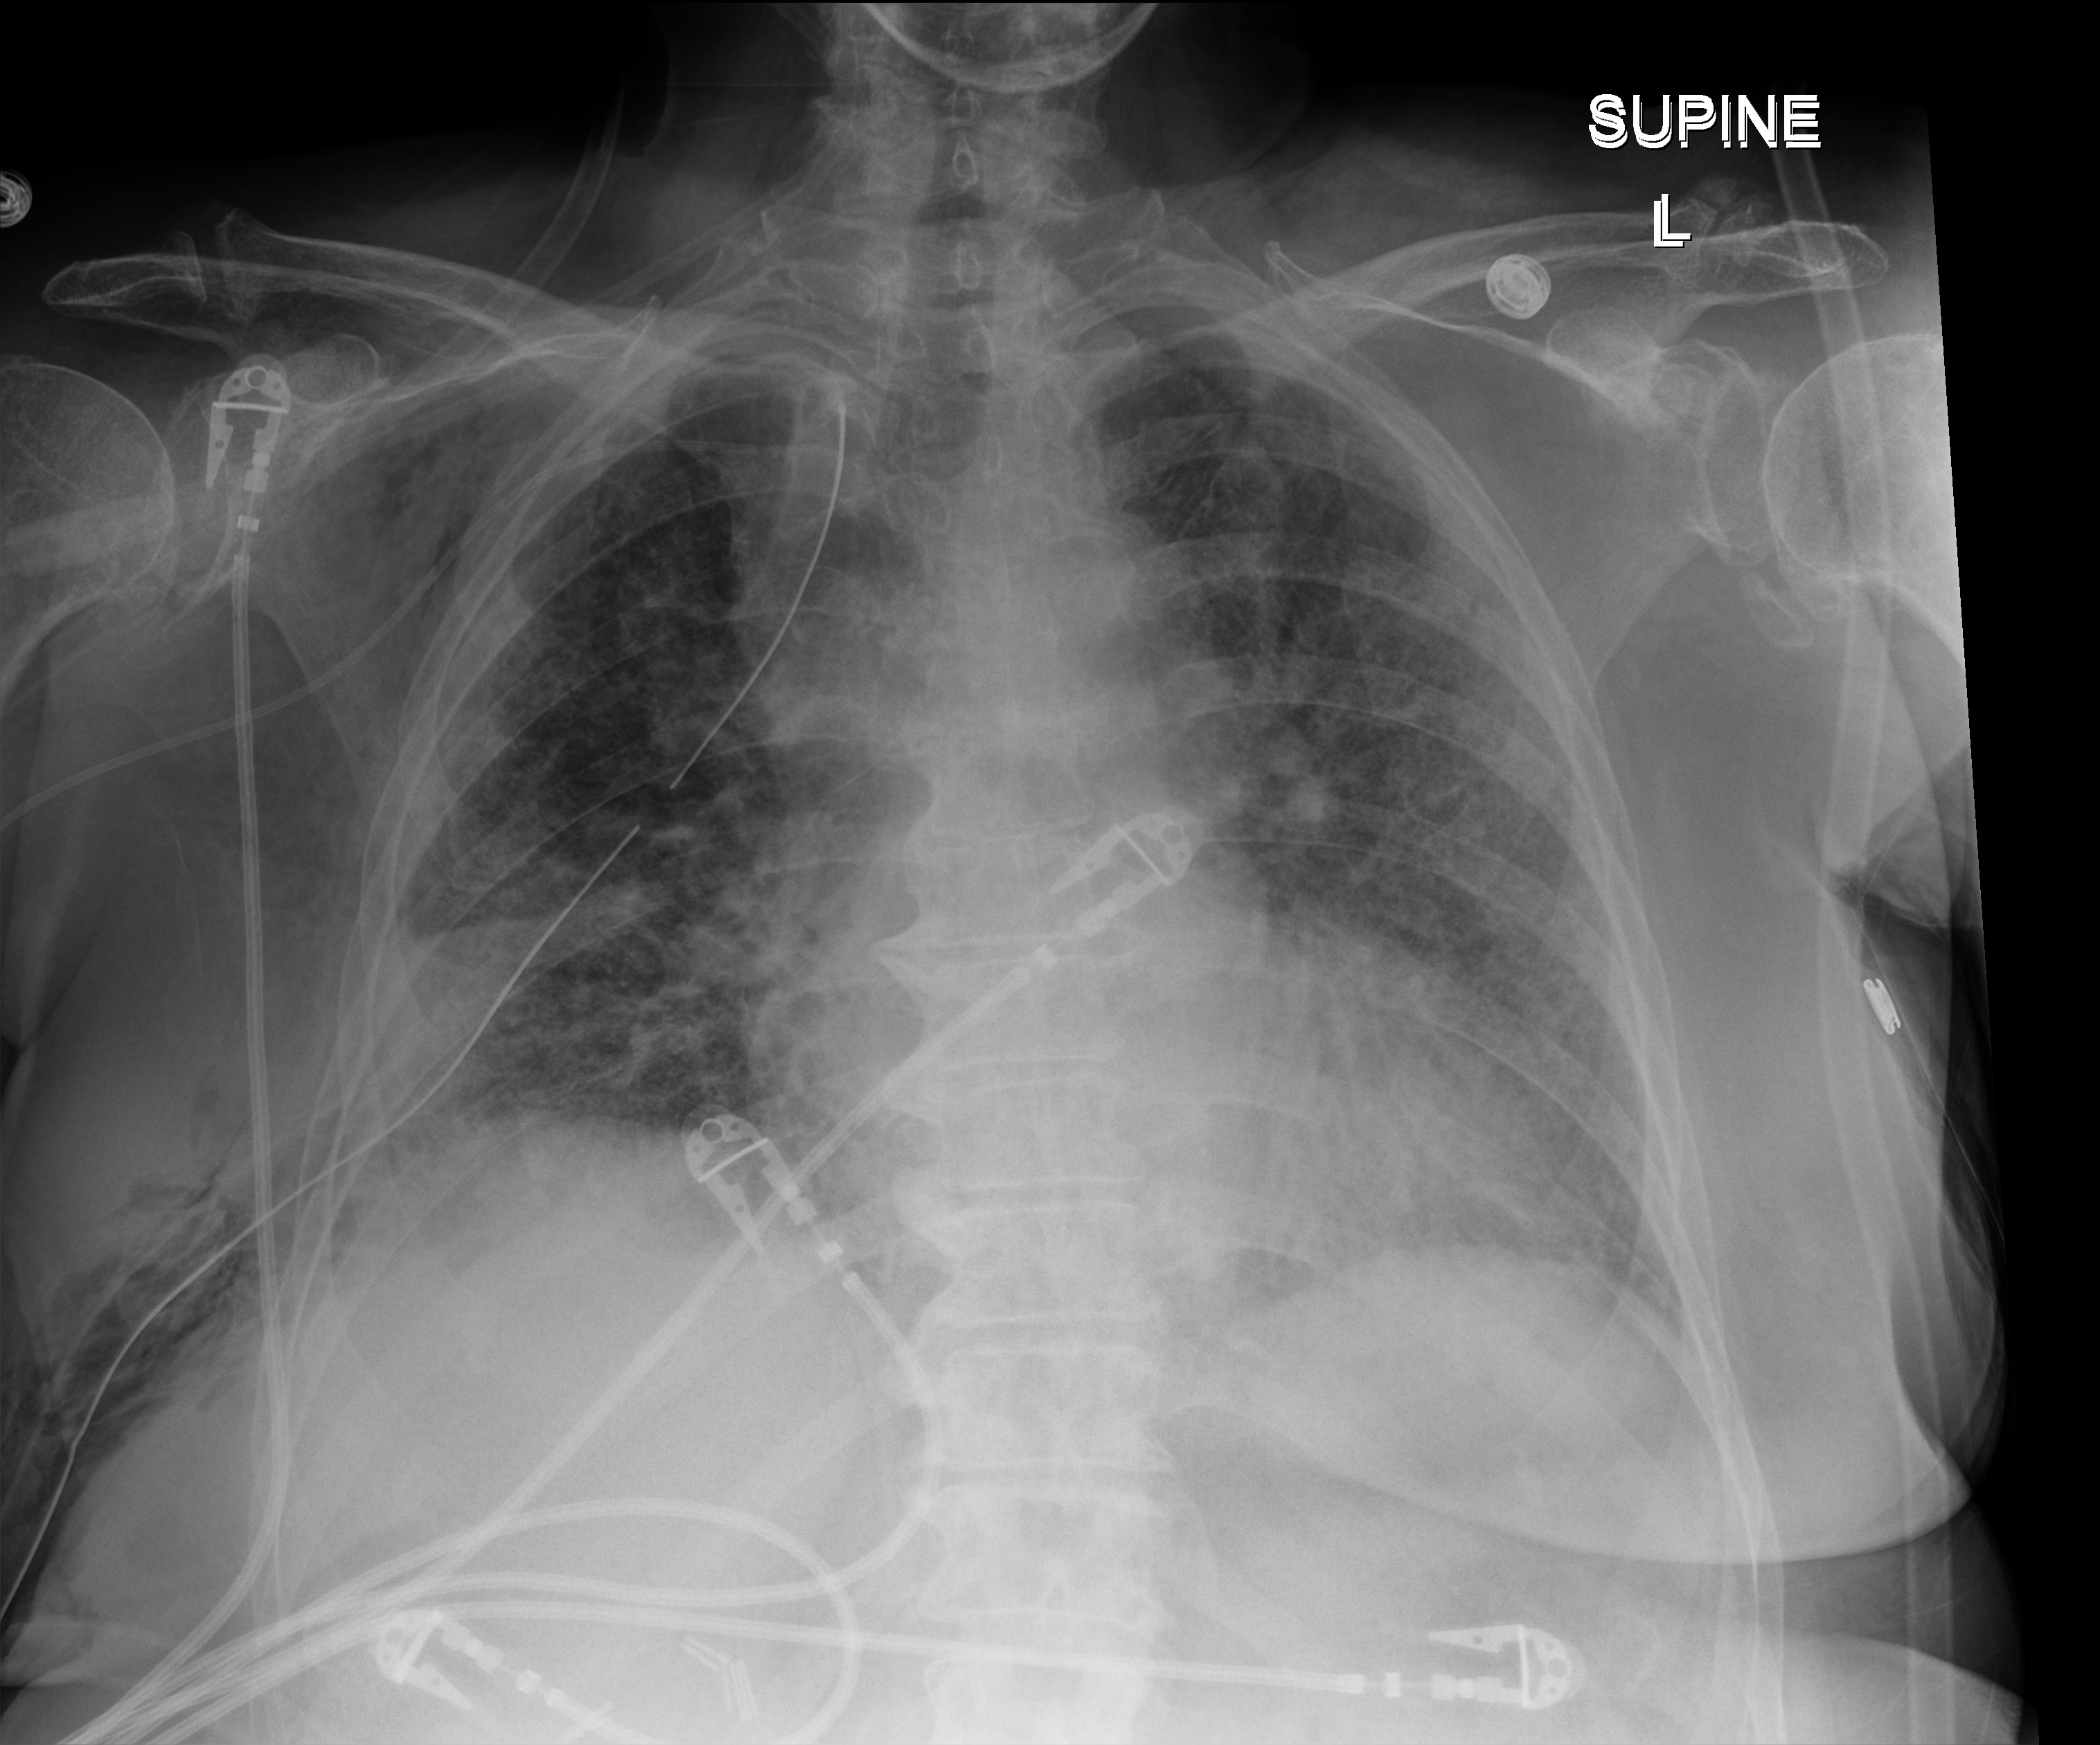
Chest radiograph. Patient hospitalised with COVID-19; female, aged 75–90 years.
Hospital-stay facts (about this admission, not read from this image; timing relative to this image not recorded):
- admitted to intensive care during this hospital stay: no